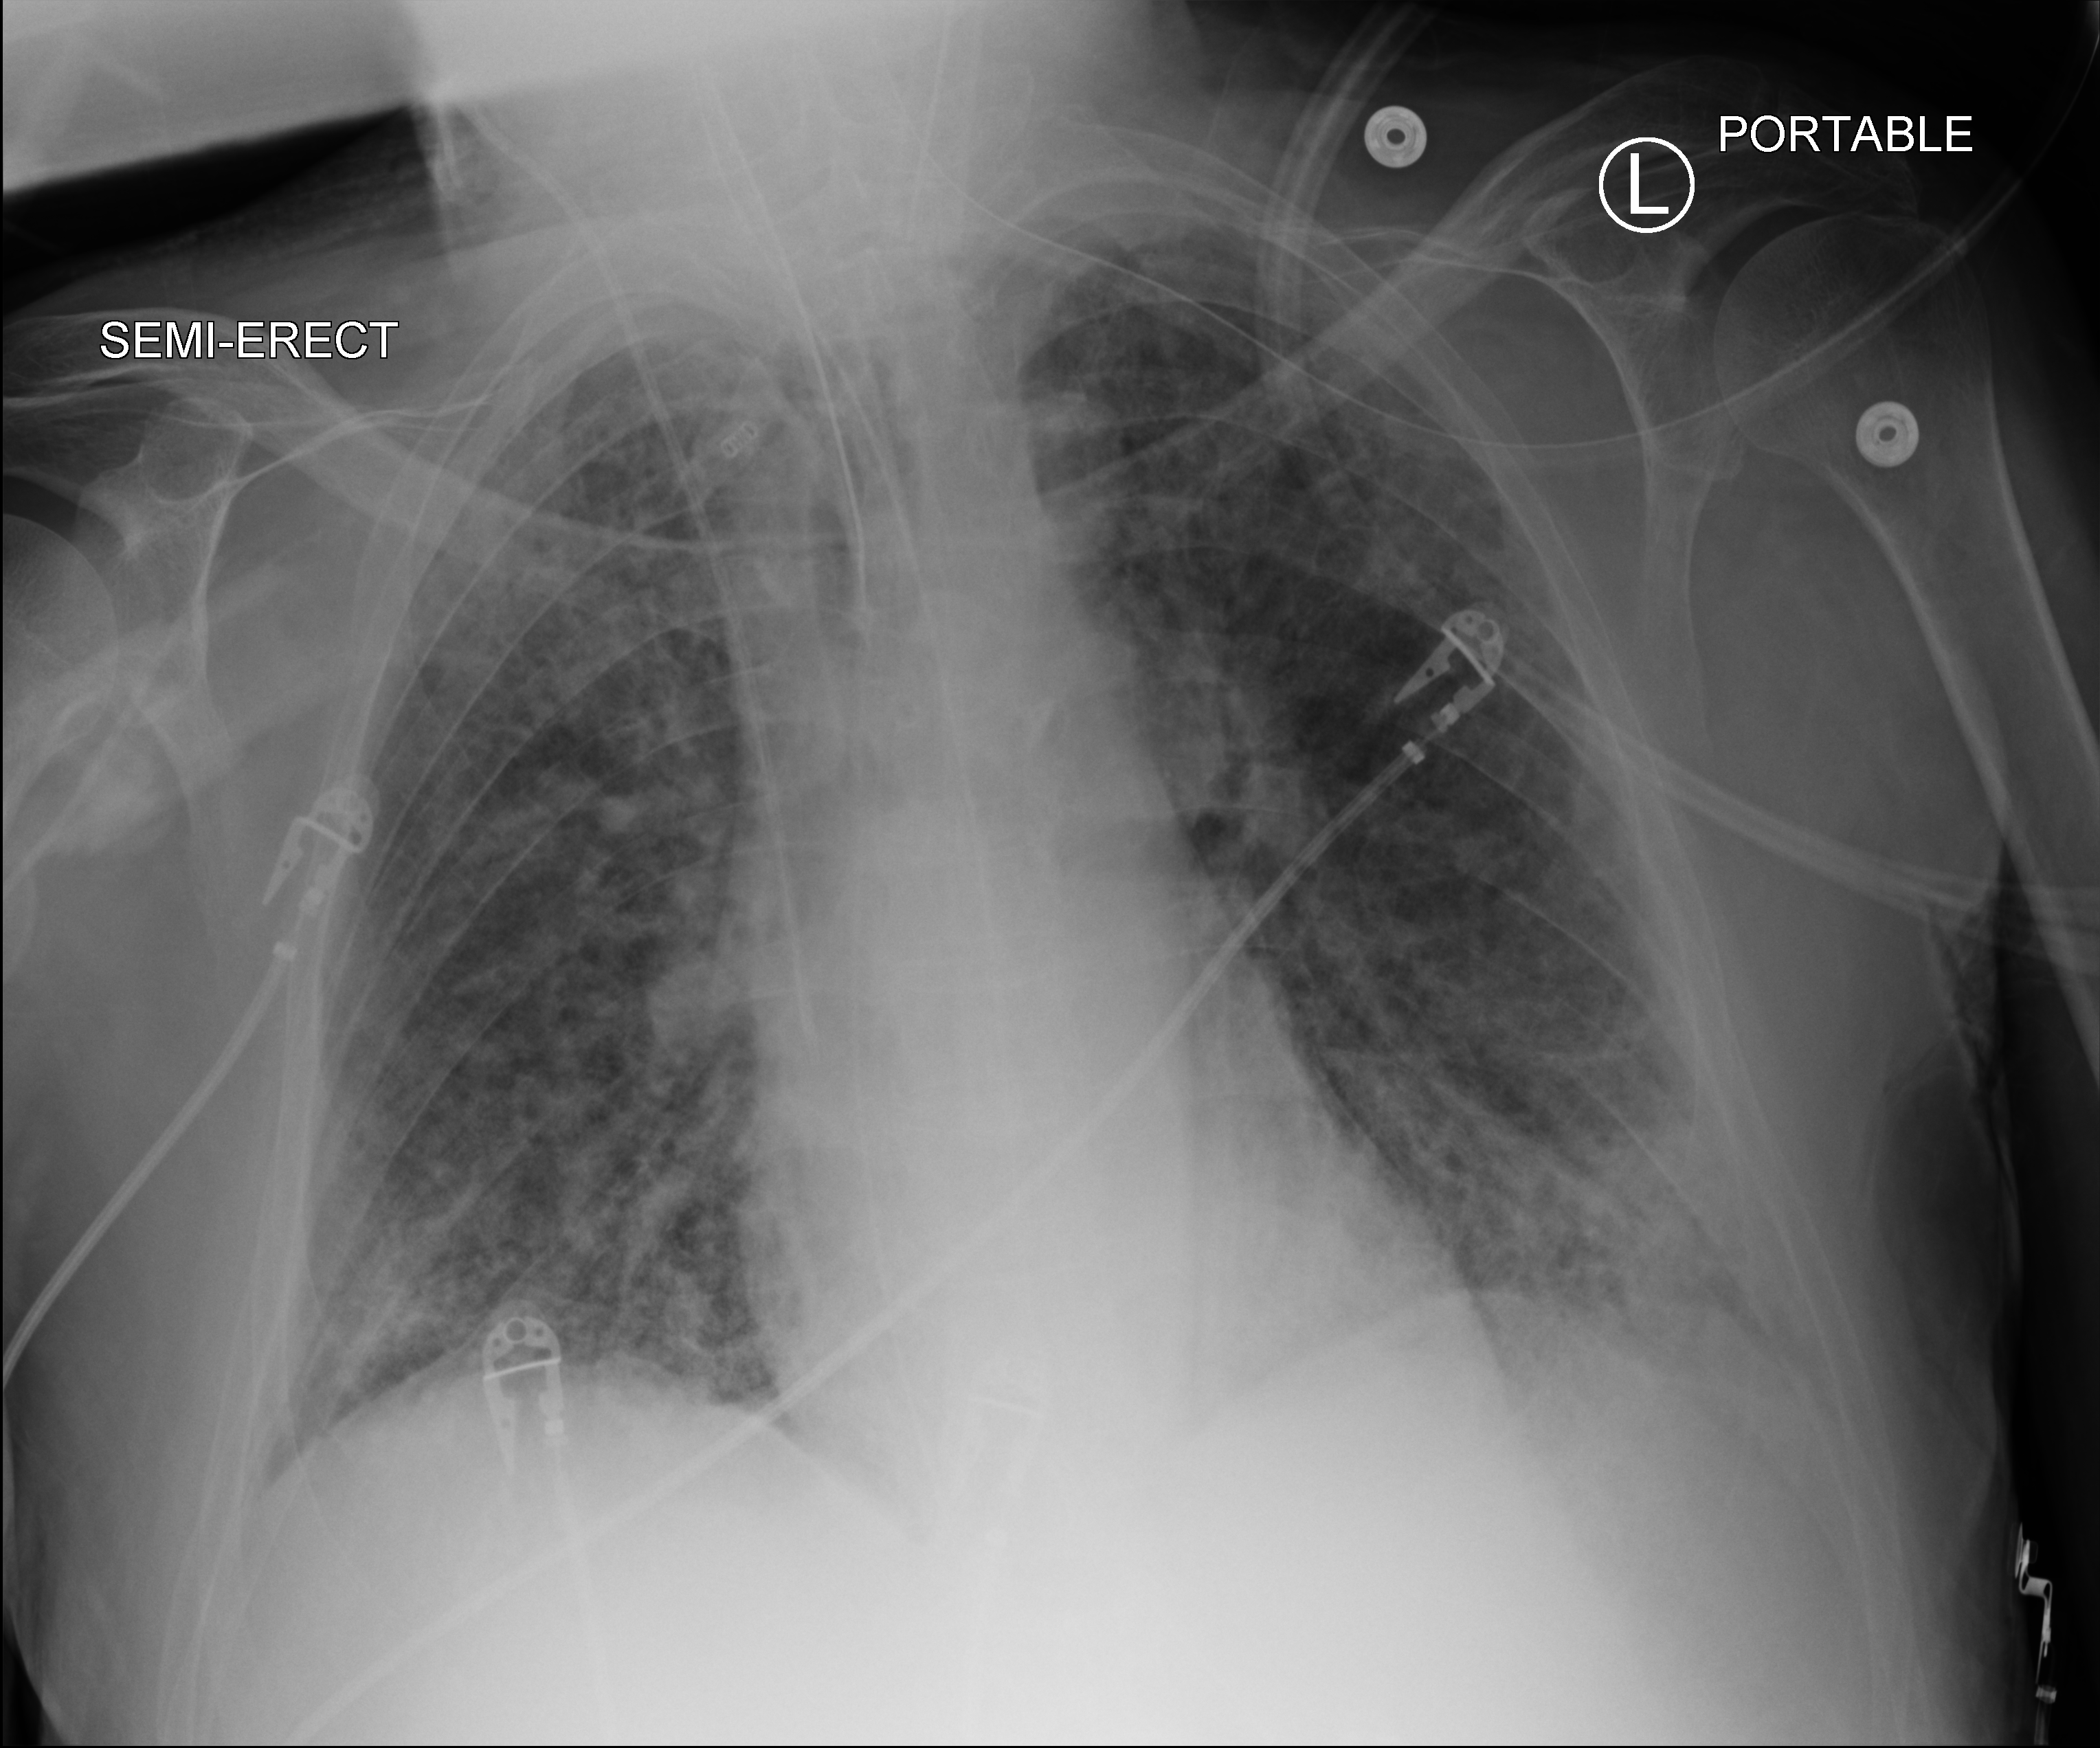
Bedside chest radiograph (computed radiography), anteroposterior (AP) projection. Patient hospitalised with COVID-19; male, aged 60–74 years.
Admission-level facts for this patient (not findings on this image; timing relative to this image not recorded): length of hospital stay: 25 days; admitted to intensive care during this hospital stay: yes.